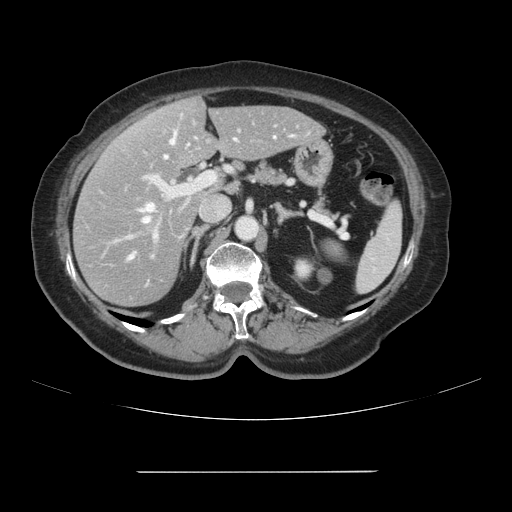
Contrast-enhanced abdominal CT, one axial slice; slice 56 of 111 in the series (ordered by position); 120 kVp; intravenous contrast given; soft-tissue window (W 400 / L 40 HU); 2.5 mm slice thickness; 512 × 512 image matrix, field of view 400 × 400 mm. Female patient, age 74 years. From the clinical record (not read from this slice): diagnosis: colorectal cancer liver metastases, imaged before liver resection; multiple liver metastases: yes; largest metastasis: 1.1 cm; disease in both lobes: yes.
Structures marked on this image (manually delineated by an expert):
- hepatic veins: bounding box (x1, y1, x2, y2) in pixels: (130, 133, 176, 258)
- liver: (74, 99, 322, 306)
- planned liver remnant (the part of the liver to remain after resection): (145, 99, 322, 167)
- portal vein (with intrahepatic branches): (122, 121, 299, 243)